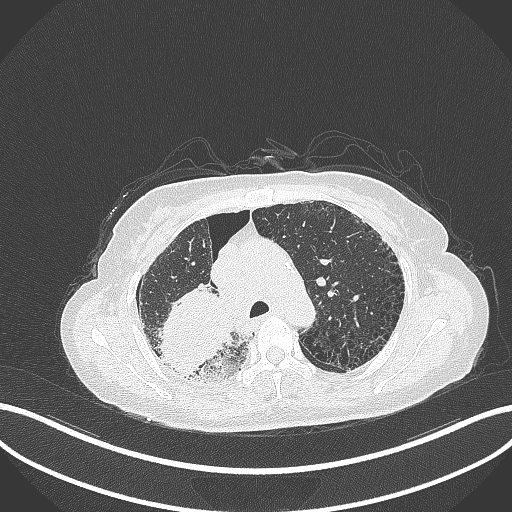
Chest CT, one axial slice. Position 246 of 408 along the scan axis. 120 kVp. Lung window (W 1500 / L -600 HU). 1 mm slice thickness. 512 × 512 image matrix. Female patient, age 64 years. From the clinical record (not read from this slice): clinical TNM (as recorded): T3 N3 M0.
Structures marked on this image (rectangle marked by the reading radiologist):
- lung tumour (recorded histology: squamous cell carcinoma): box from (x=155, y=281) to (x=235, y=379) px